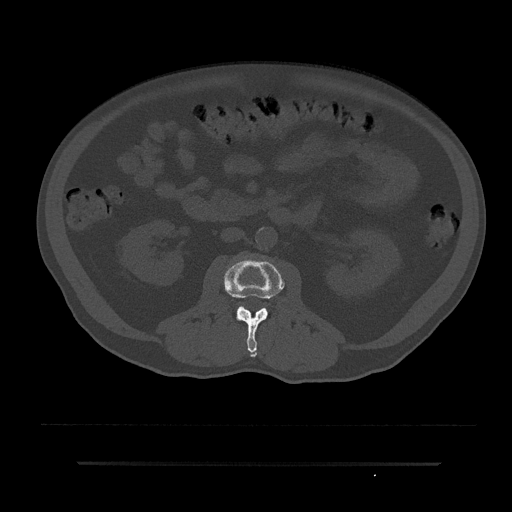
CT including the spine, one axial slice. Position 53 of 797 along the scan axis. 120 kVp. Bone window (W 1800 / L 400 HU). 0.5 mm slice thickness. 512 × 512 image matrix, field of view 464 × 464 mm. Patient: male, 59 years. From the clinical record (not read from this slice): primary cancer: bile ducts.
Outlined on this slice (semi-automatically segmented with operator editing):
- L2 vertebra: box from (x=222, y=258) to (x=285, y=357) px